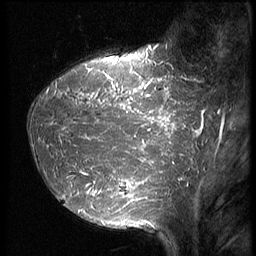
Breast MRI (dynamic contrast-enhanced), one sagittal slice. Slice 18 of 64 in the series (ordered by position). 3 images stored at this slice position (order not interpretable as contrast timing). 1.5 T. TE 4.2 ms, TR 9 ms. 256 × 256 image matrix, field of view 180 × 180 mm. Patient: female, 39 years. Case-level facts recorded for this patient, not image findings: setting: breast cancer imaged before/during neoadjuvant chemotherapy; receptor status: HER2-positive.
Outlined on this slice (semi-automatic segmentation, software-assisted and operator-edited):
- analysis volume of interest (the breast-tissue region the enhancement analysis was run in; not a lesion): box from (x=27, y=47) to (x=210, y=239) px
- tumour enhancement mask (voxels above the 140 % enhancement threshold inside the analysis volume of interest): (x=58, y=47)–(x=210, y=212)